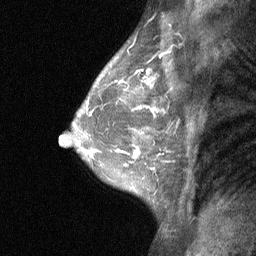
Breast MRI (dynamic contrast-enhanced), one sagittal slice. Position 44 of 64 along the scan axis. Dynamic contrast-enhanced study with each time point stored as its own series, time point 2 of 3 at this slice position (early post-contrast, ordered by acquisition time). 1.5 T. TE 4.8 ms, TR 27 ms. 2 mm slice thickness. 256 × 256 image matrix. Patient: female, 47 years. Case-level facts recorded for this patient, not image findings: setting: breast cancer imaged before/during neoadjuvant chemotherapy; receptor status: HR-positive, HER2-negative.
Structures marked on this image (semi-automatic segmentation, software-assisted and operator-edited):
- analysis volume of interest (the breast-tissue region the enhancement analysis was run in; not a lesion): bounding box <104,138,165,198> (left, top, right, bottom; pixels)
- tumour enhancement mask (voxels above the 90 % enhancement threshold inside the analysis volume of interest): <134,149,140,158>